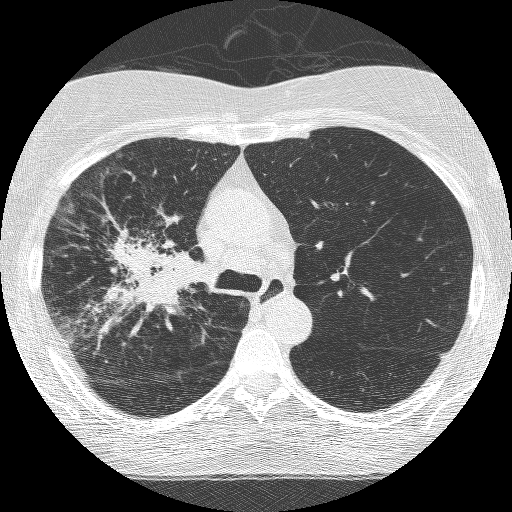
Axial slice from a low-dose chest CT screening exam, third annual screen, lung window (W 1500 / L -600 HU), slice 175 of 253 in the series. Female participant, aged 64 years at enrolment. Former smoker at enrolment.
• Lesion marked by an expert reader, bounding box [x1, y1, x2, y2] px = [90, 221, 206, 337].
• Reader record for this screening exam (exam-level; its link to the box is not recorded): non-calcified nodule or mass ≥4 mm, right upper lobe, 49 × 43 mm, spiculated (stellate) margins, soft tissue attenuation, pre-existing on the prior screen: yes; interval growth: yes.
• Participant outcome: lung cancer diagnosed 7 days after this screen — adenocarcinoma, NOS, right upper lobe, right middle lobe, right hilum, stage IV (AJCC 6th edition), 85 mm at pathology.